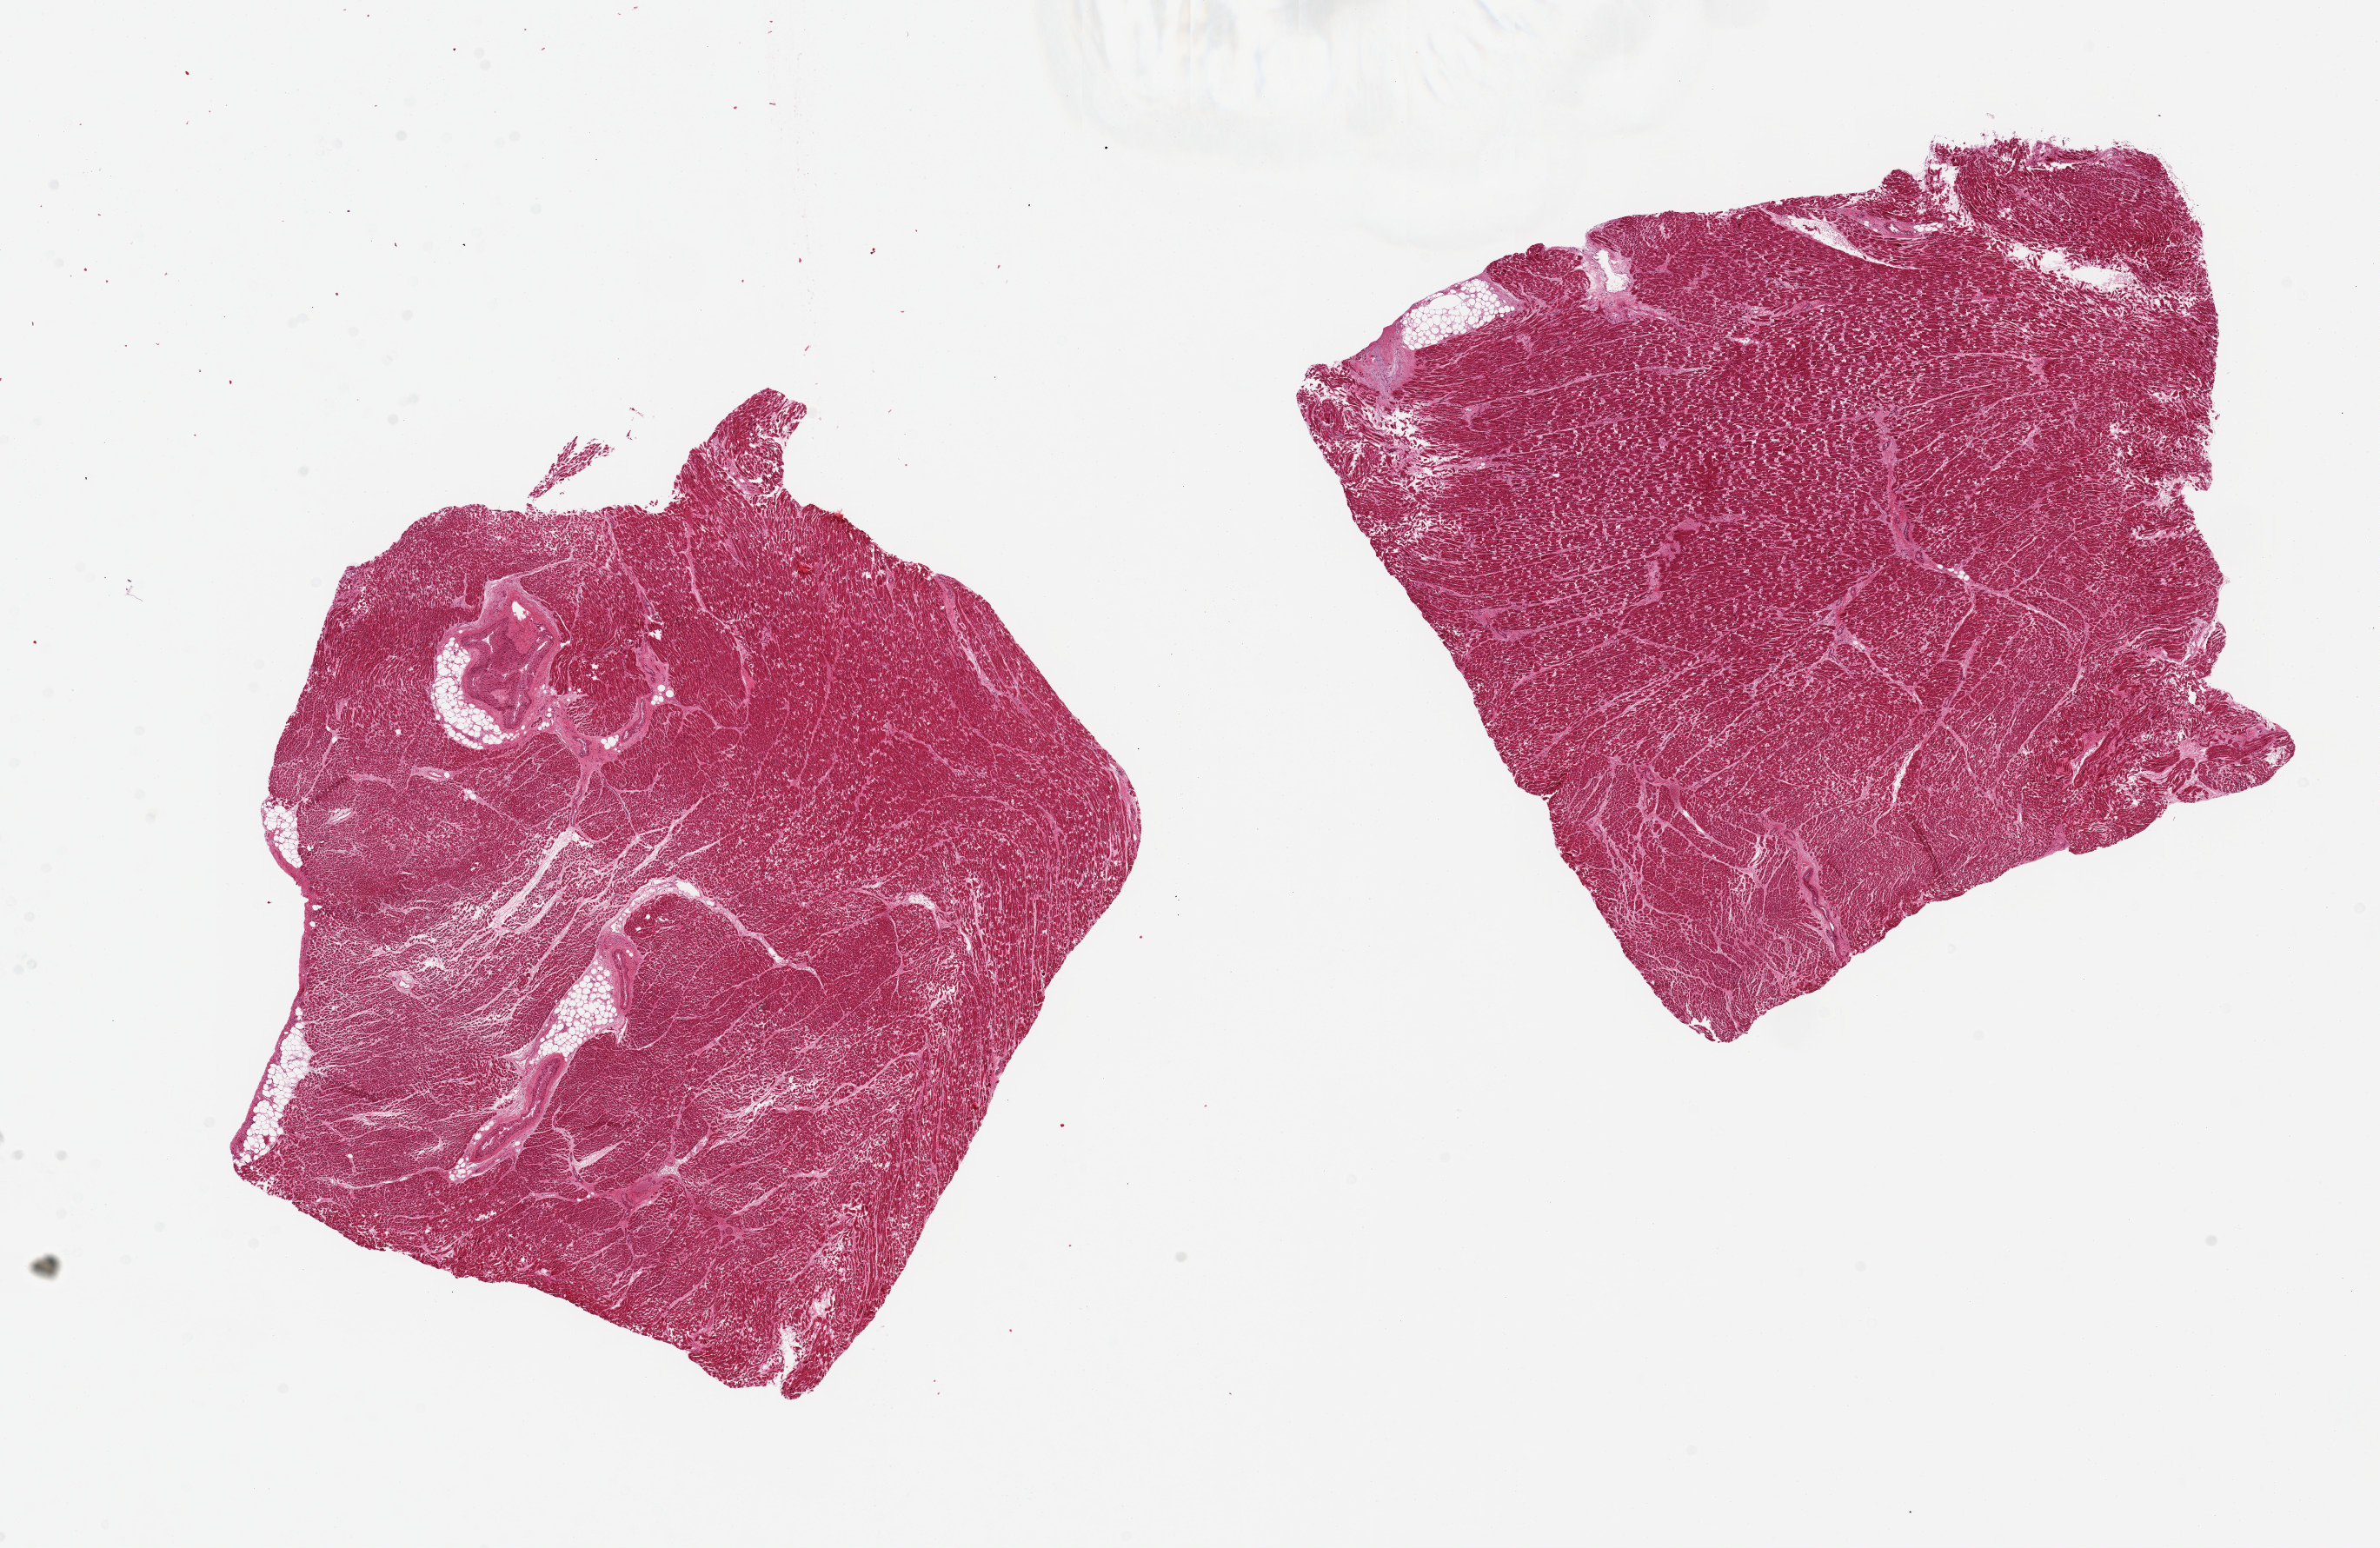
Whole-slide image, hematoxylin and eosin (H&E) stain — whole scanned area (about 21.7 x 14.1 mm, acquisition: 20x scan) shown as a low-resolution overview. PAXgene-fixed paraffin-embedded (PFPE) section. Sampled site (target tissue): heart. Tissue donor sample.
Reviewer comment on this tissue sample: 2 pieces, 7.5x7 & 8x7mm; minimal ischemic change but badly autolyzed.